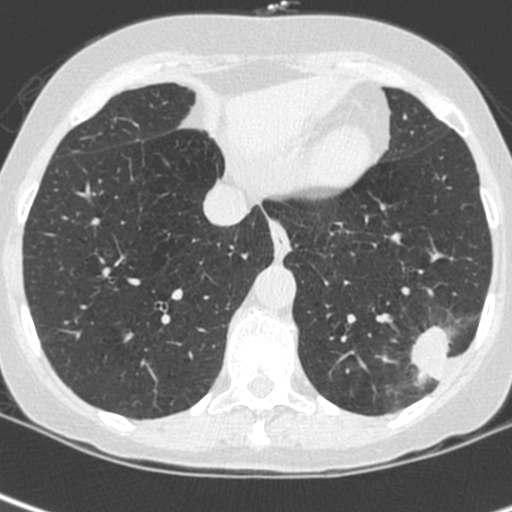
Chest CT (low-dose screening protocol), one axial image; baseline annual screen; lung window (W 1500 / L -600 HU); 1.3 mm slice thickness; standard (soft-tissue) reconstruction kernel (C); slice 170 of 252 in the series; 512 × 512 image matrix. Female, age 56 years at enrolment. Current smoker at enrolment.
Expert-annotated lung lesion, bounding box [x1, y1, x2, y2] px = [406, 319, 475, 388]. The exam's reader record, not a measurement of the box and not confirmed to be the same lesion: non-calcified nodule or mass ≥4 mm, left lower lobe, 37 × 29 mm, spiculated (stellate) margins, ground glass attenuation. Later outcome: lung cancer diagnosed 91 days after this screen — squamous cell carcinoma, NOS, left lower lobe, poorly differentiated (G3), stage IIIA (AJCC 6th edition), 35 mm at pathology.